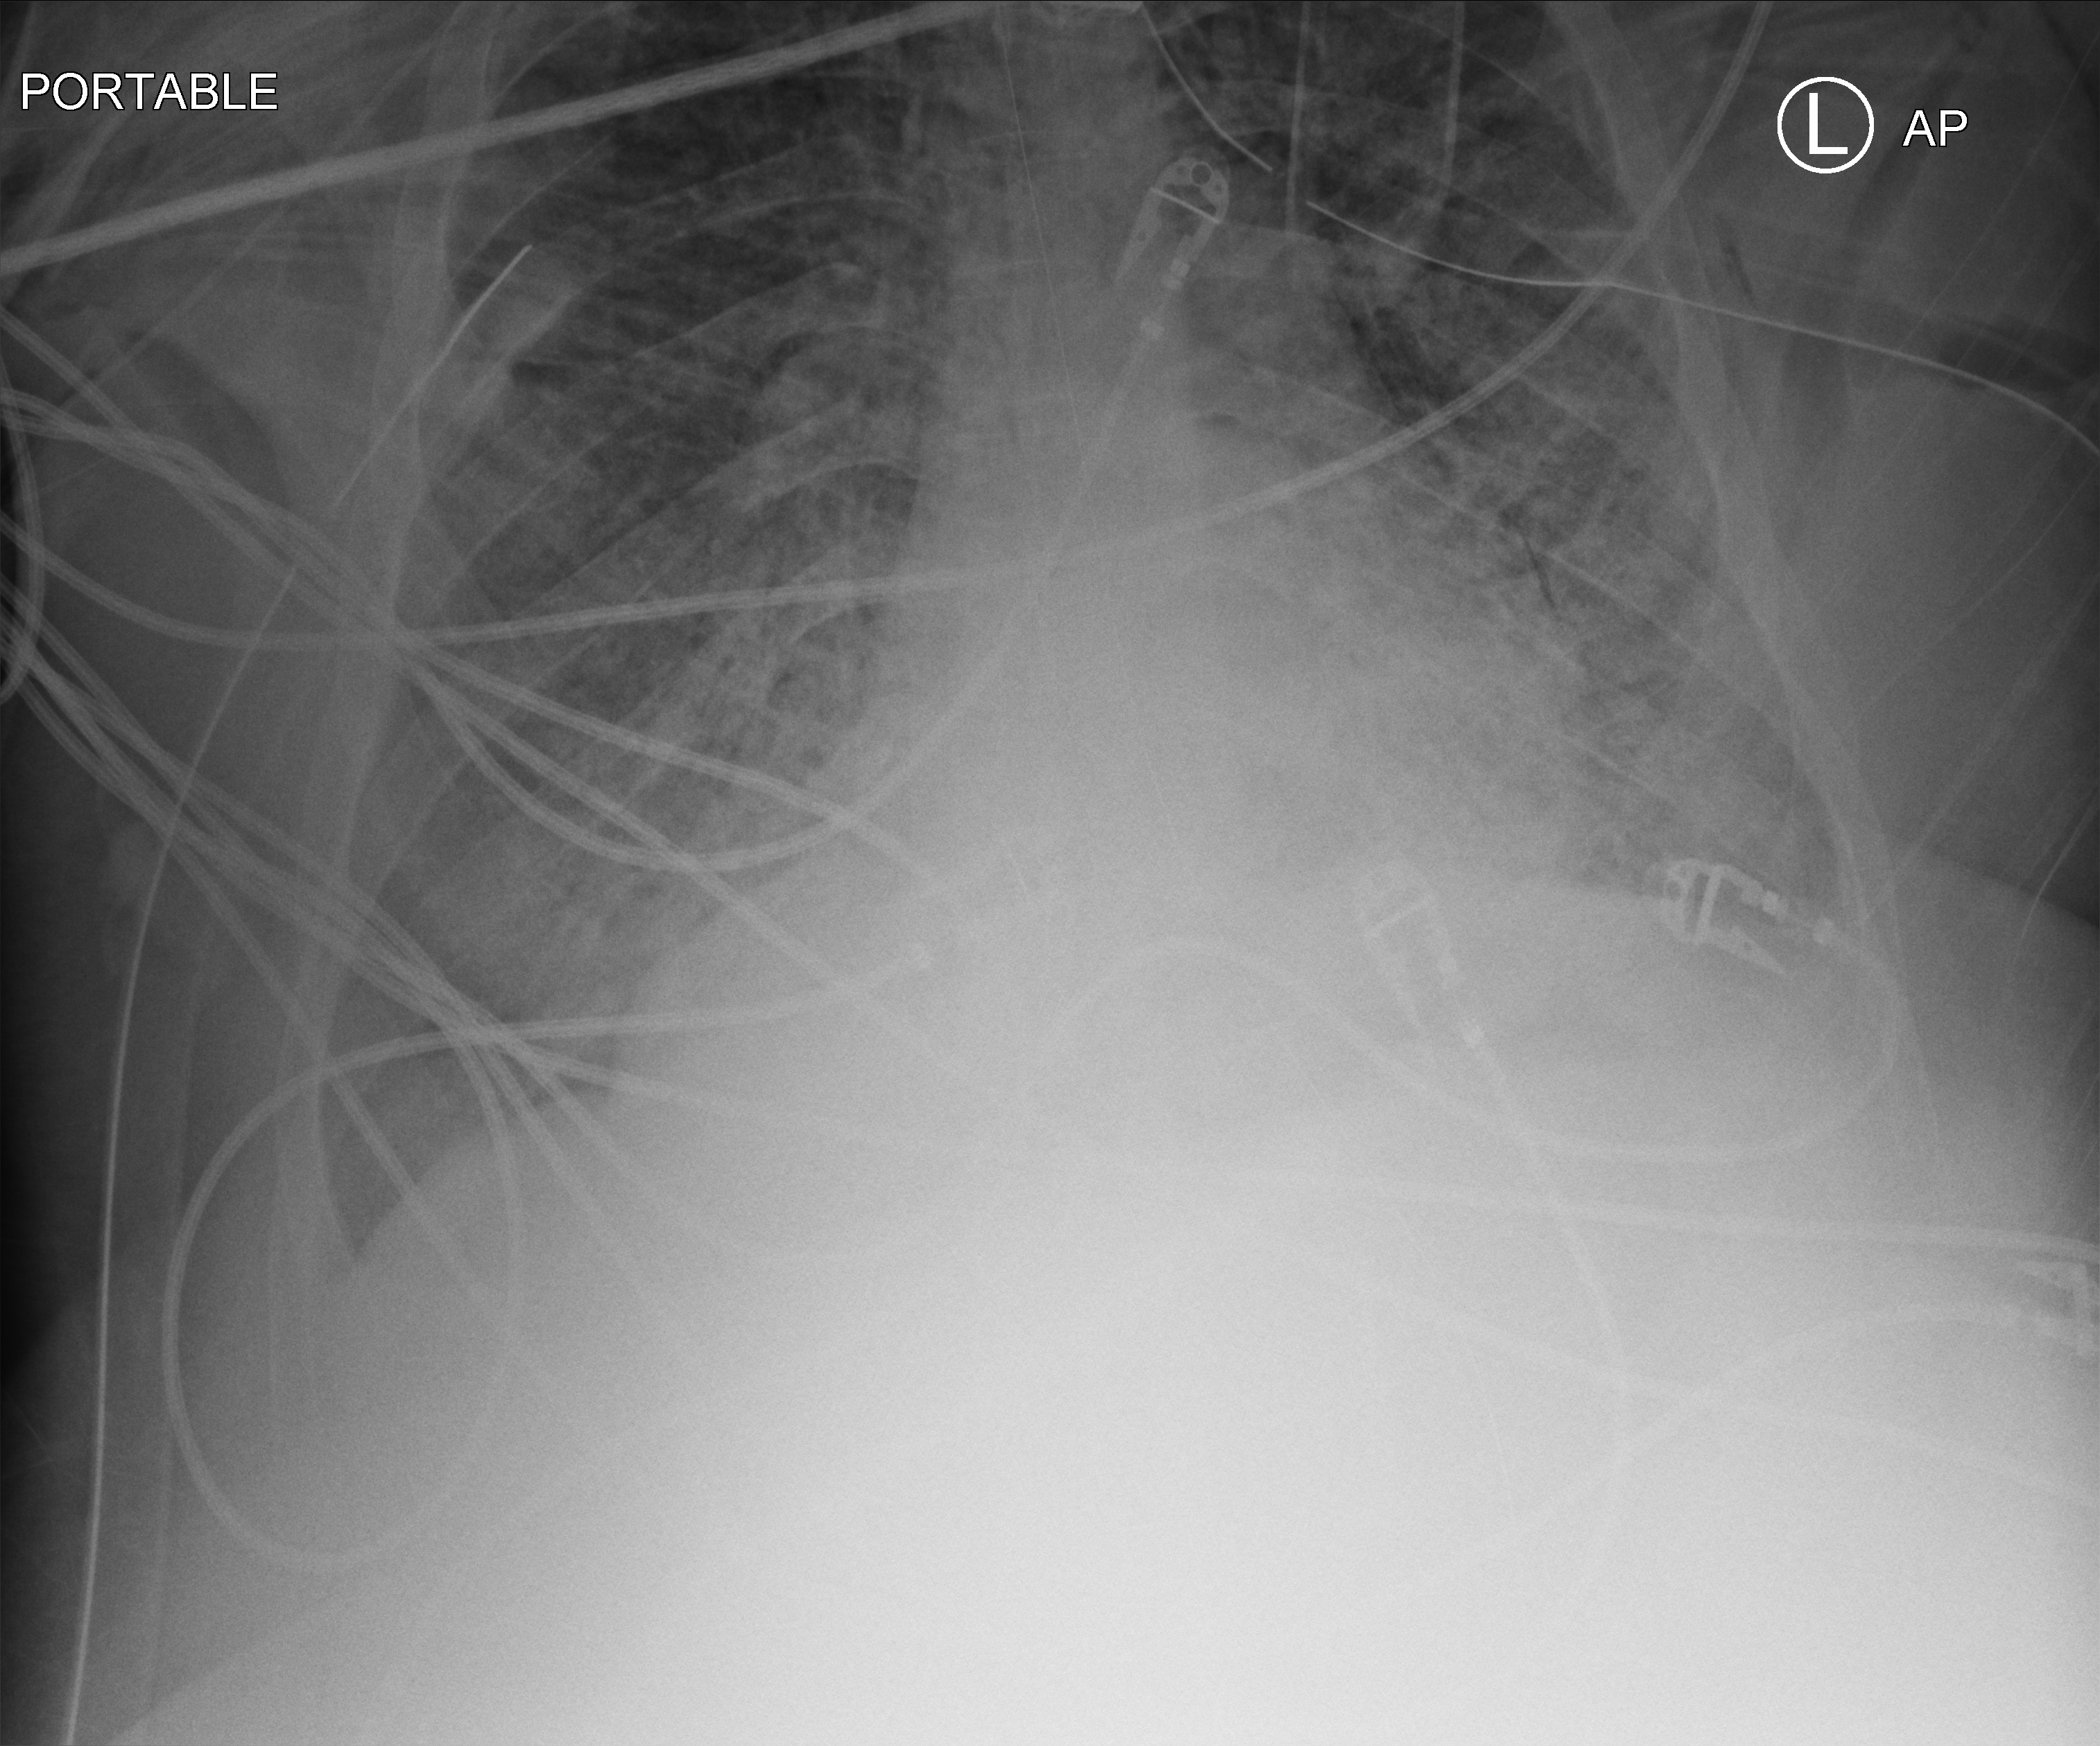
Portable chest radiograph. Patient hospitalised with COVID-19, aged 18–59 years.
Admission-level facts for this patient (not findings on this image; timing relative to this image not recorded): mechanically ventilated during this hospital stay: yes.